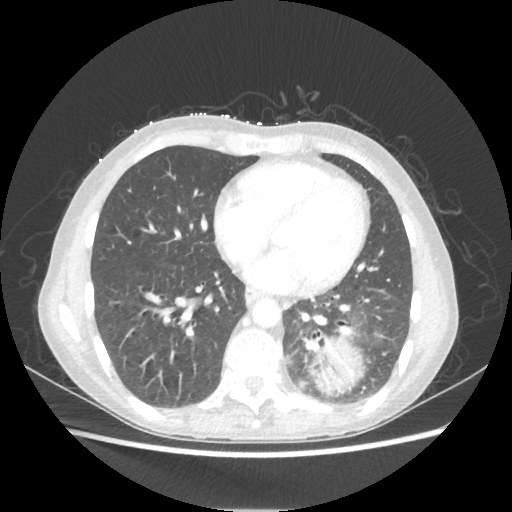
Chest CT, one axial slice; slice 86 of 221 in the series (ordered by position); reconstruction kernel STANDARD; lung window (W 1500 / L -600 HU); 1.25 mm slice thickness; 512 × 512 image matrix, field of view 360 × 360 mm. Patient: female, 53 years. From the clinical record (not read from this slice): clinical TNM (as recorded): T3 N0 M0.
Annotated regions visible in this slice (rectangle marked by the reading radiologist):
- lung tumour (recorded histology: adenocarcinoma): bounding box [x1, y1, x2, y2] px = [307, 337, 364, 396]